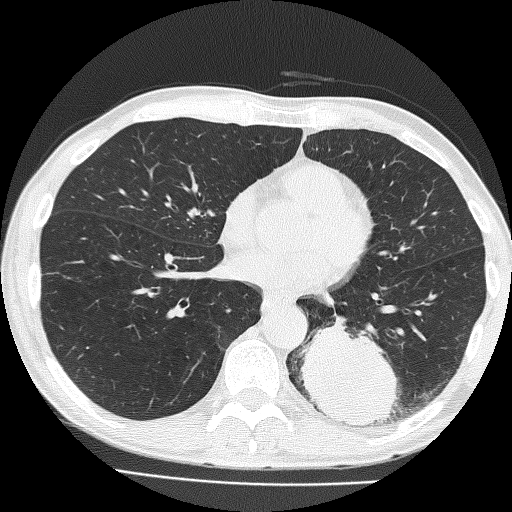
Chest CT (low-dose screening protocol), one axial image. Baseline screening round. Lung window (W 1500 / L -600 HU). 2 mm slice thickness. Lung (sharp) reconstruction kernel (FC51). 512 × 512 image matrix. Male, age 58 years at enrolment. Current smoker at enrolment.
Lesion marked by an expert reader, bounding box [x1, y1, x2, y2] px = [299, 309, 421, 434]. The screening reader recorded 2 non-calcified nodules or masses ≥4 mm on this exam; which of them this box marks is not recorded. Official screen result: positive, change unspecified: nodule(s) >= 4 mm or enlarging nodule(s), mass(es), or other non-specific abnormalities suspicious for lung cancer. Later outcome: lung cancer diagnosed 39 days after this screen — non-small cell carcinoma, left lower lobe, poorly differentiated (G3), stage IV (AJCC 6th edition), 74 mm at pathology.